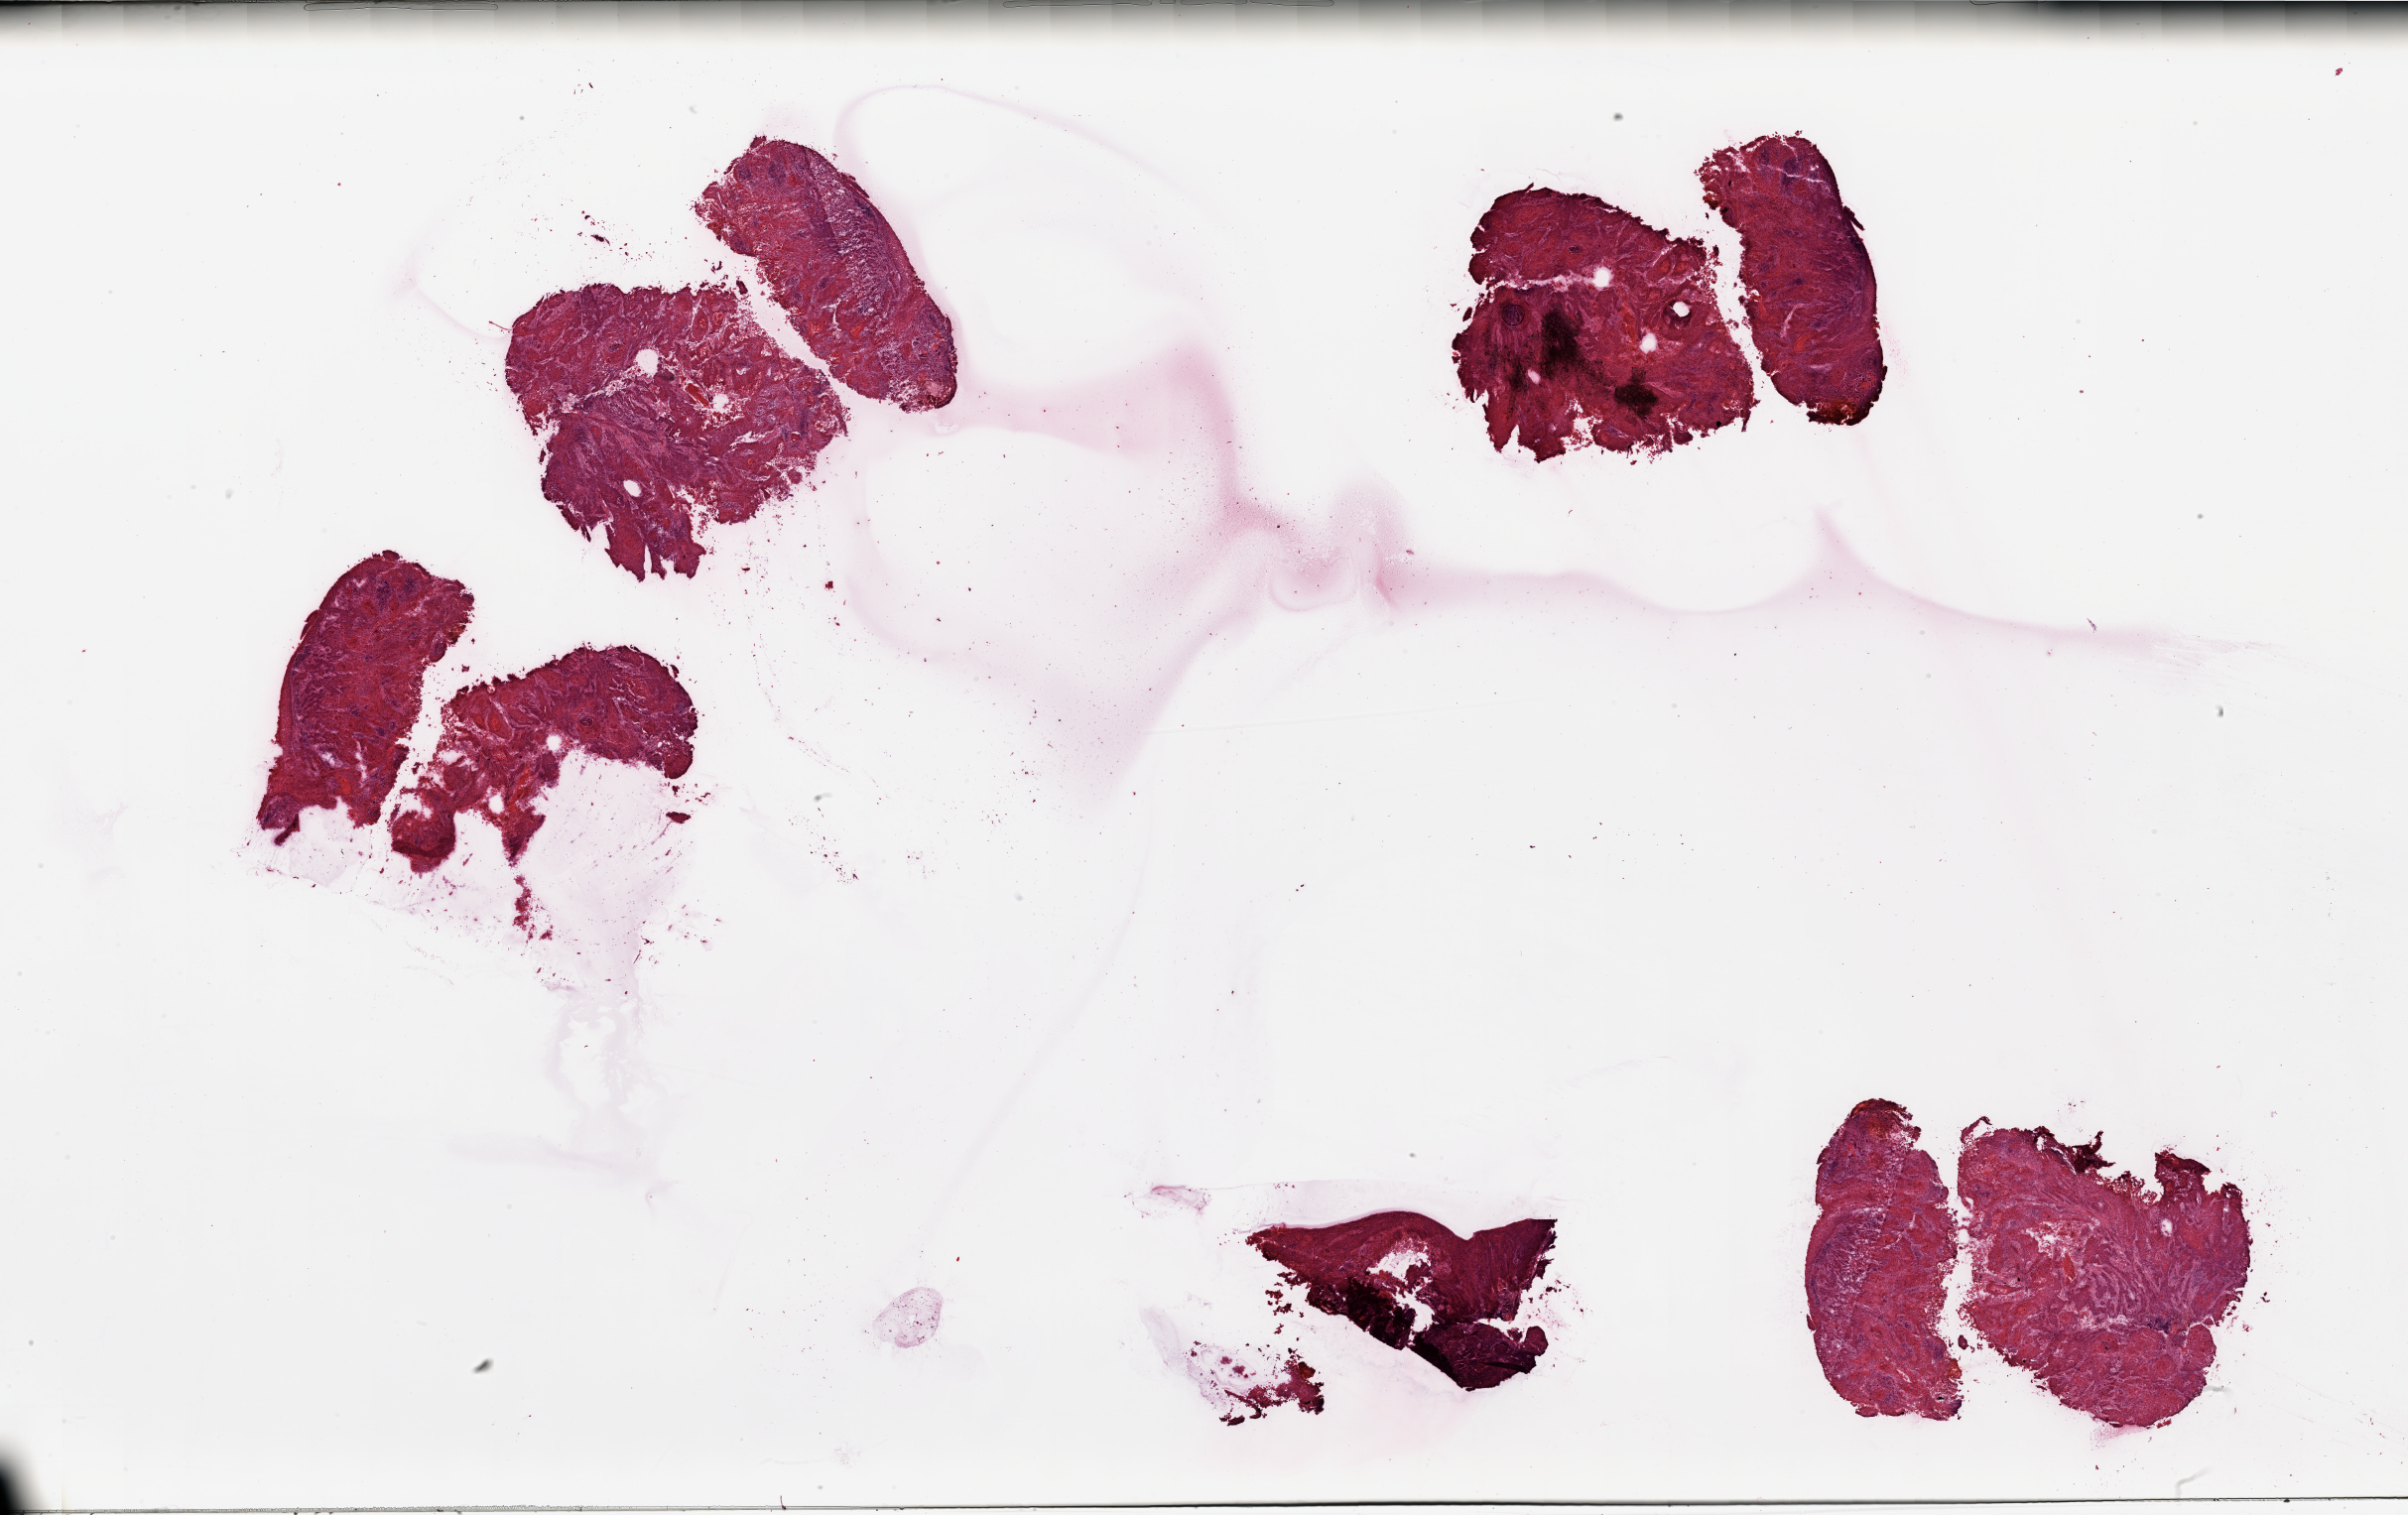
Whole-slide histology image, Hematoxylin and eosin (H&E) stained, low-resolution overview of the scanned area, about 38.4 x 24.2 mm (slide scanned at 20x). Tumour tissue sample, sampled site: larynx. 69-year-old male patient. Histologic grade: G2 (moderately differentiated). Pathologist review of this section (percent, as recorded): tumour nuclei 90%, necrosis 10%.
Primary tumour site (as recorded): larynx. AJCC pathologic stage: II. Histologic diagnosis: Squamous cell carcinoma, NOS.